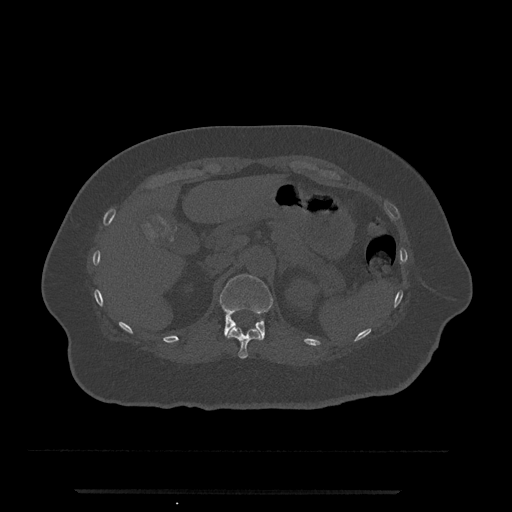
CT including the spine, one axial slice. Position 196 of 797 along the scan axis. Reconstruction kernel Br40s/3. Bone window (W 1800 / L 400 HU). 0.5 mm slice thickness. 512 × 512 image matrix. Patient: female, 51 years. From the clinical record (not read from this slice): primary cancer: neuro; vertebrae with lytic lesions (as recorded): T8.
Outlined on this slice (semi-automatic segmentation, software-assisted and operator-edited):
- T11 vertebra: bounding box (x1, y1, x2, y2) in pixels: (226, 327, 261, 359)
- T12 vertebra: (219, 274, 274, 341)